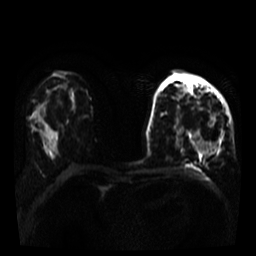
Breast MRI, one axial slice. Position 19 of 35 along the scan axis. Diffusion-weighted series; image 2 of 4 stored at this slice position (different b-values; order by instance number). 3 T. 5 mm slice thickness. 256 × 256 image matrix, field of view 320 × 320 mm. Female patient.
Structures marked on this image (expert manual segmentation):
- tumour on diffusion-weighted imaging: bounding box <194,117,223,154> (left, top, right, bottom; pixels)